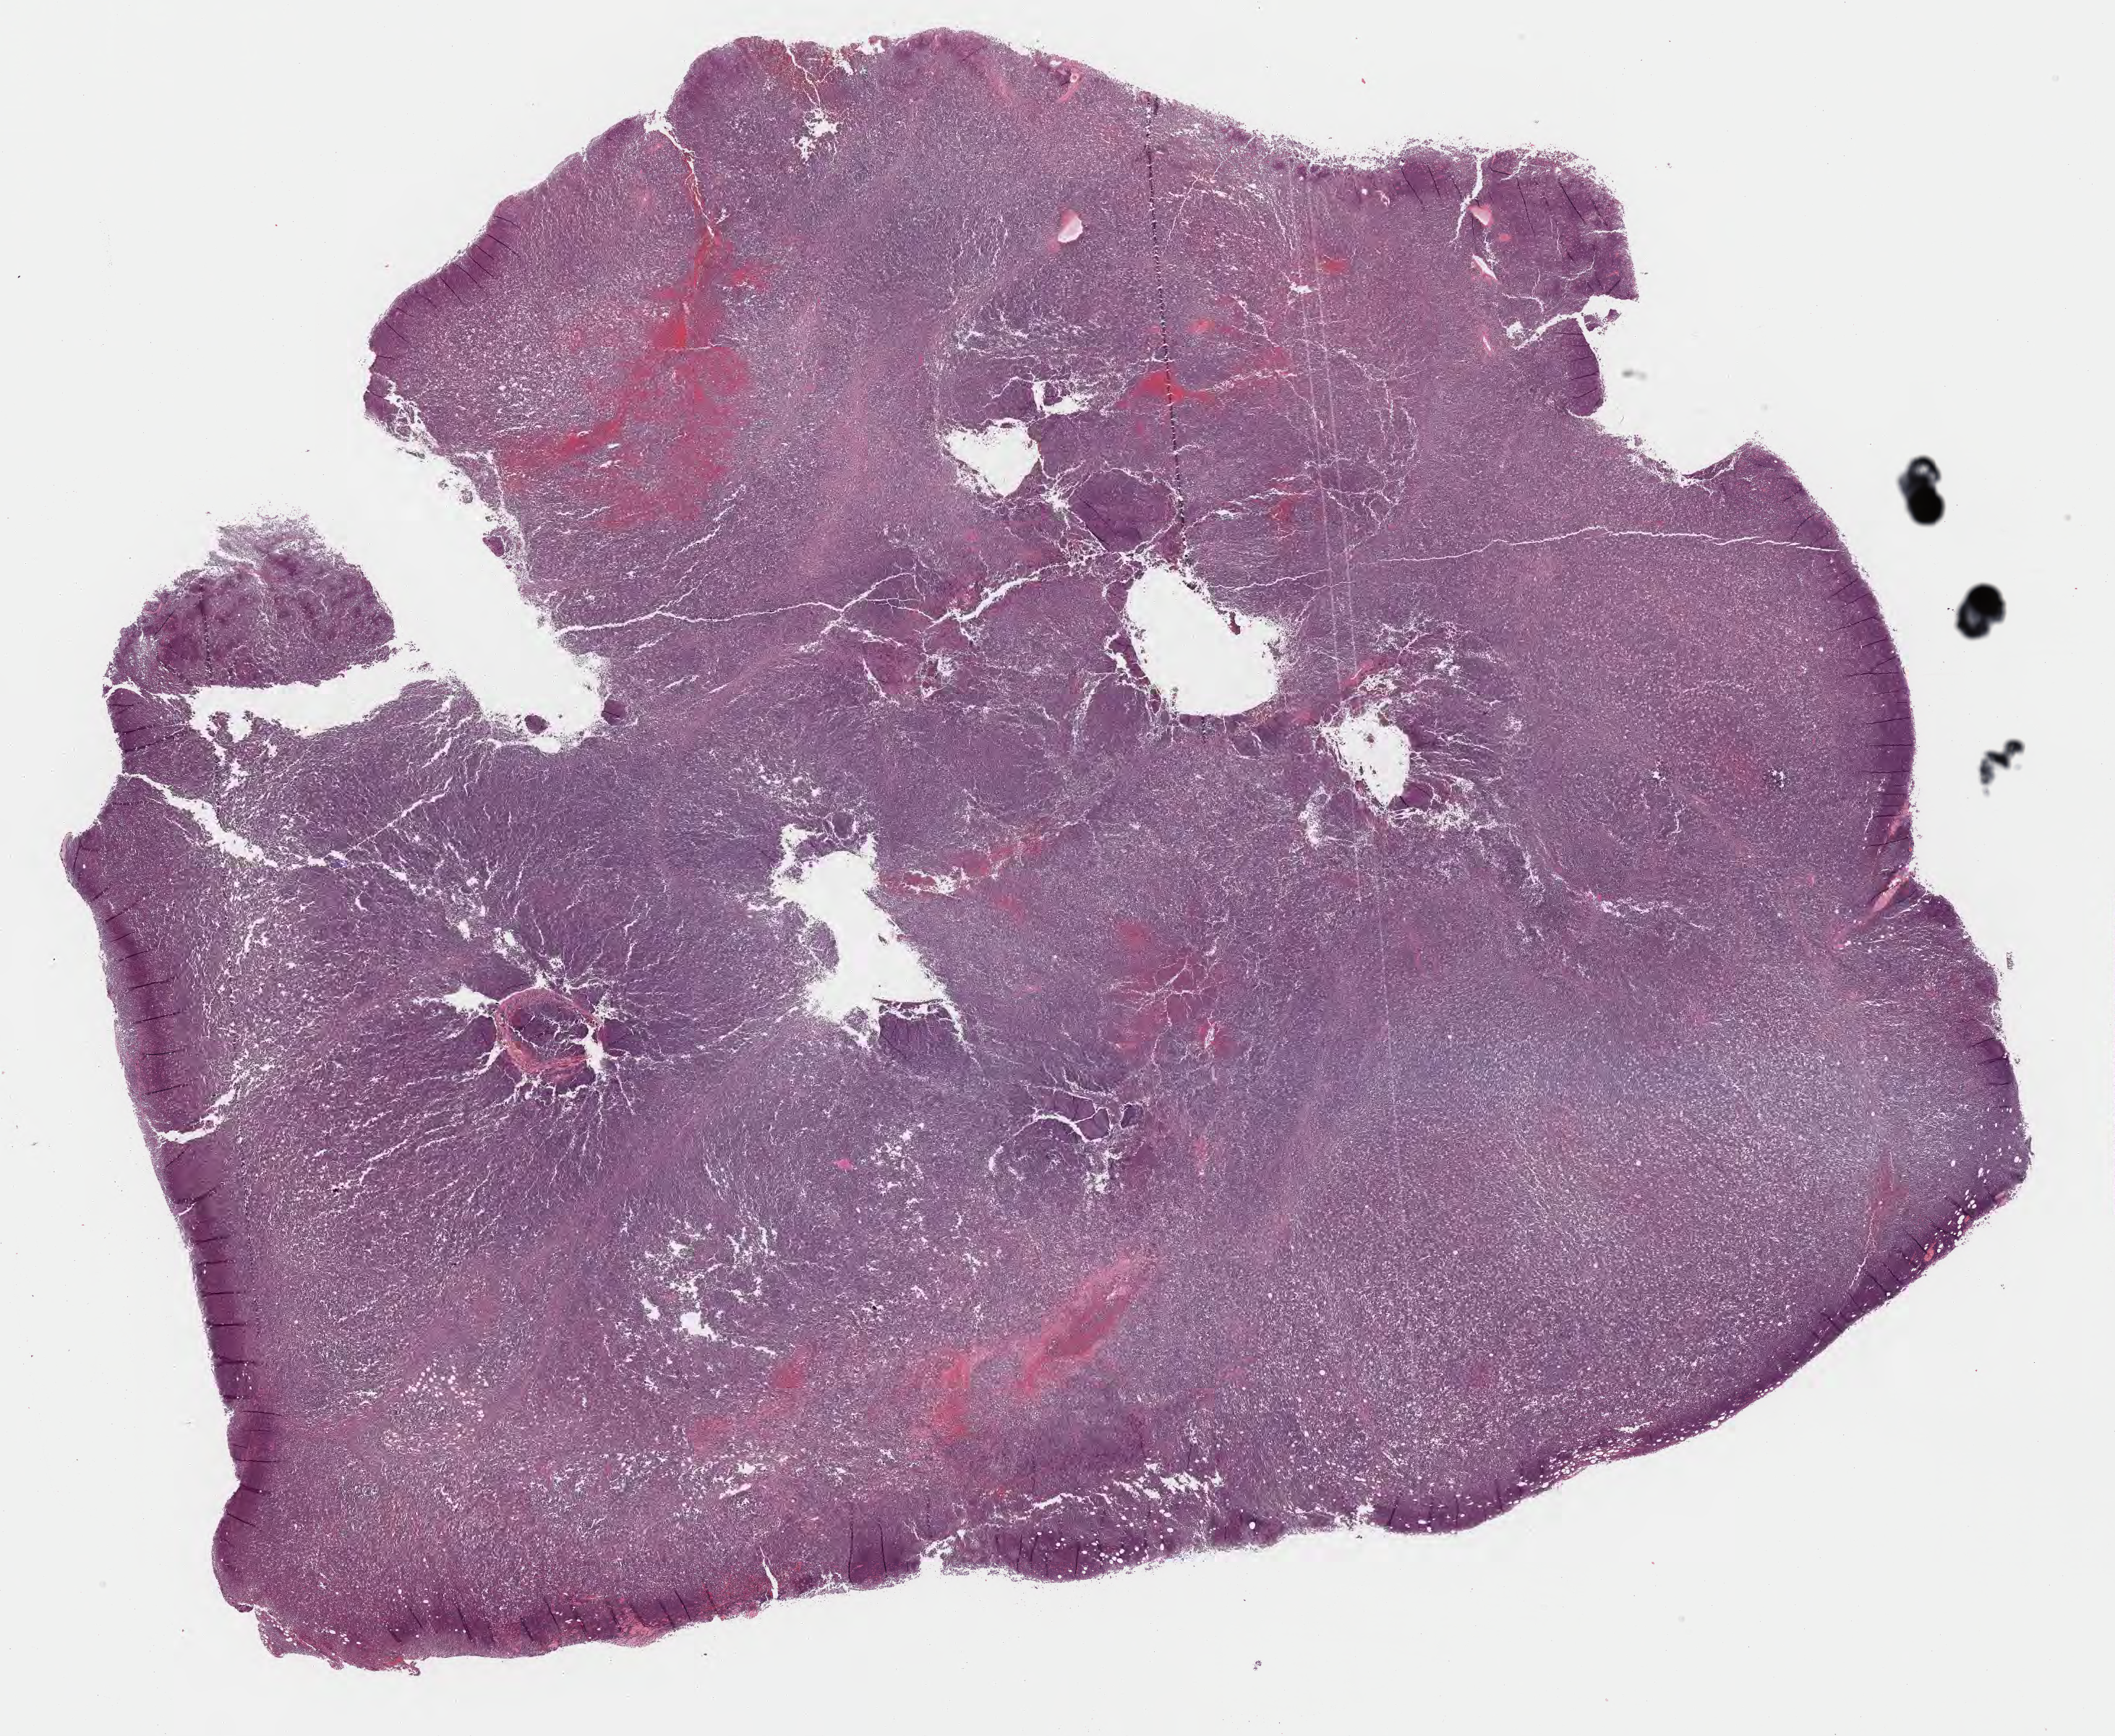
Whole-slide image, hematoxylin and eosin (H&E) stain — whole scanned area (about 23.7 x 19.4 mm) shown as a low-resolution overview. Specimen: tumor tissue. Patient sex: male.
Diagnosis: Burkitt lymphoma, NOS.